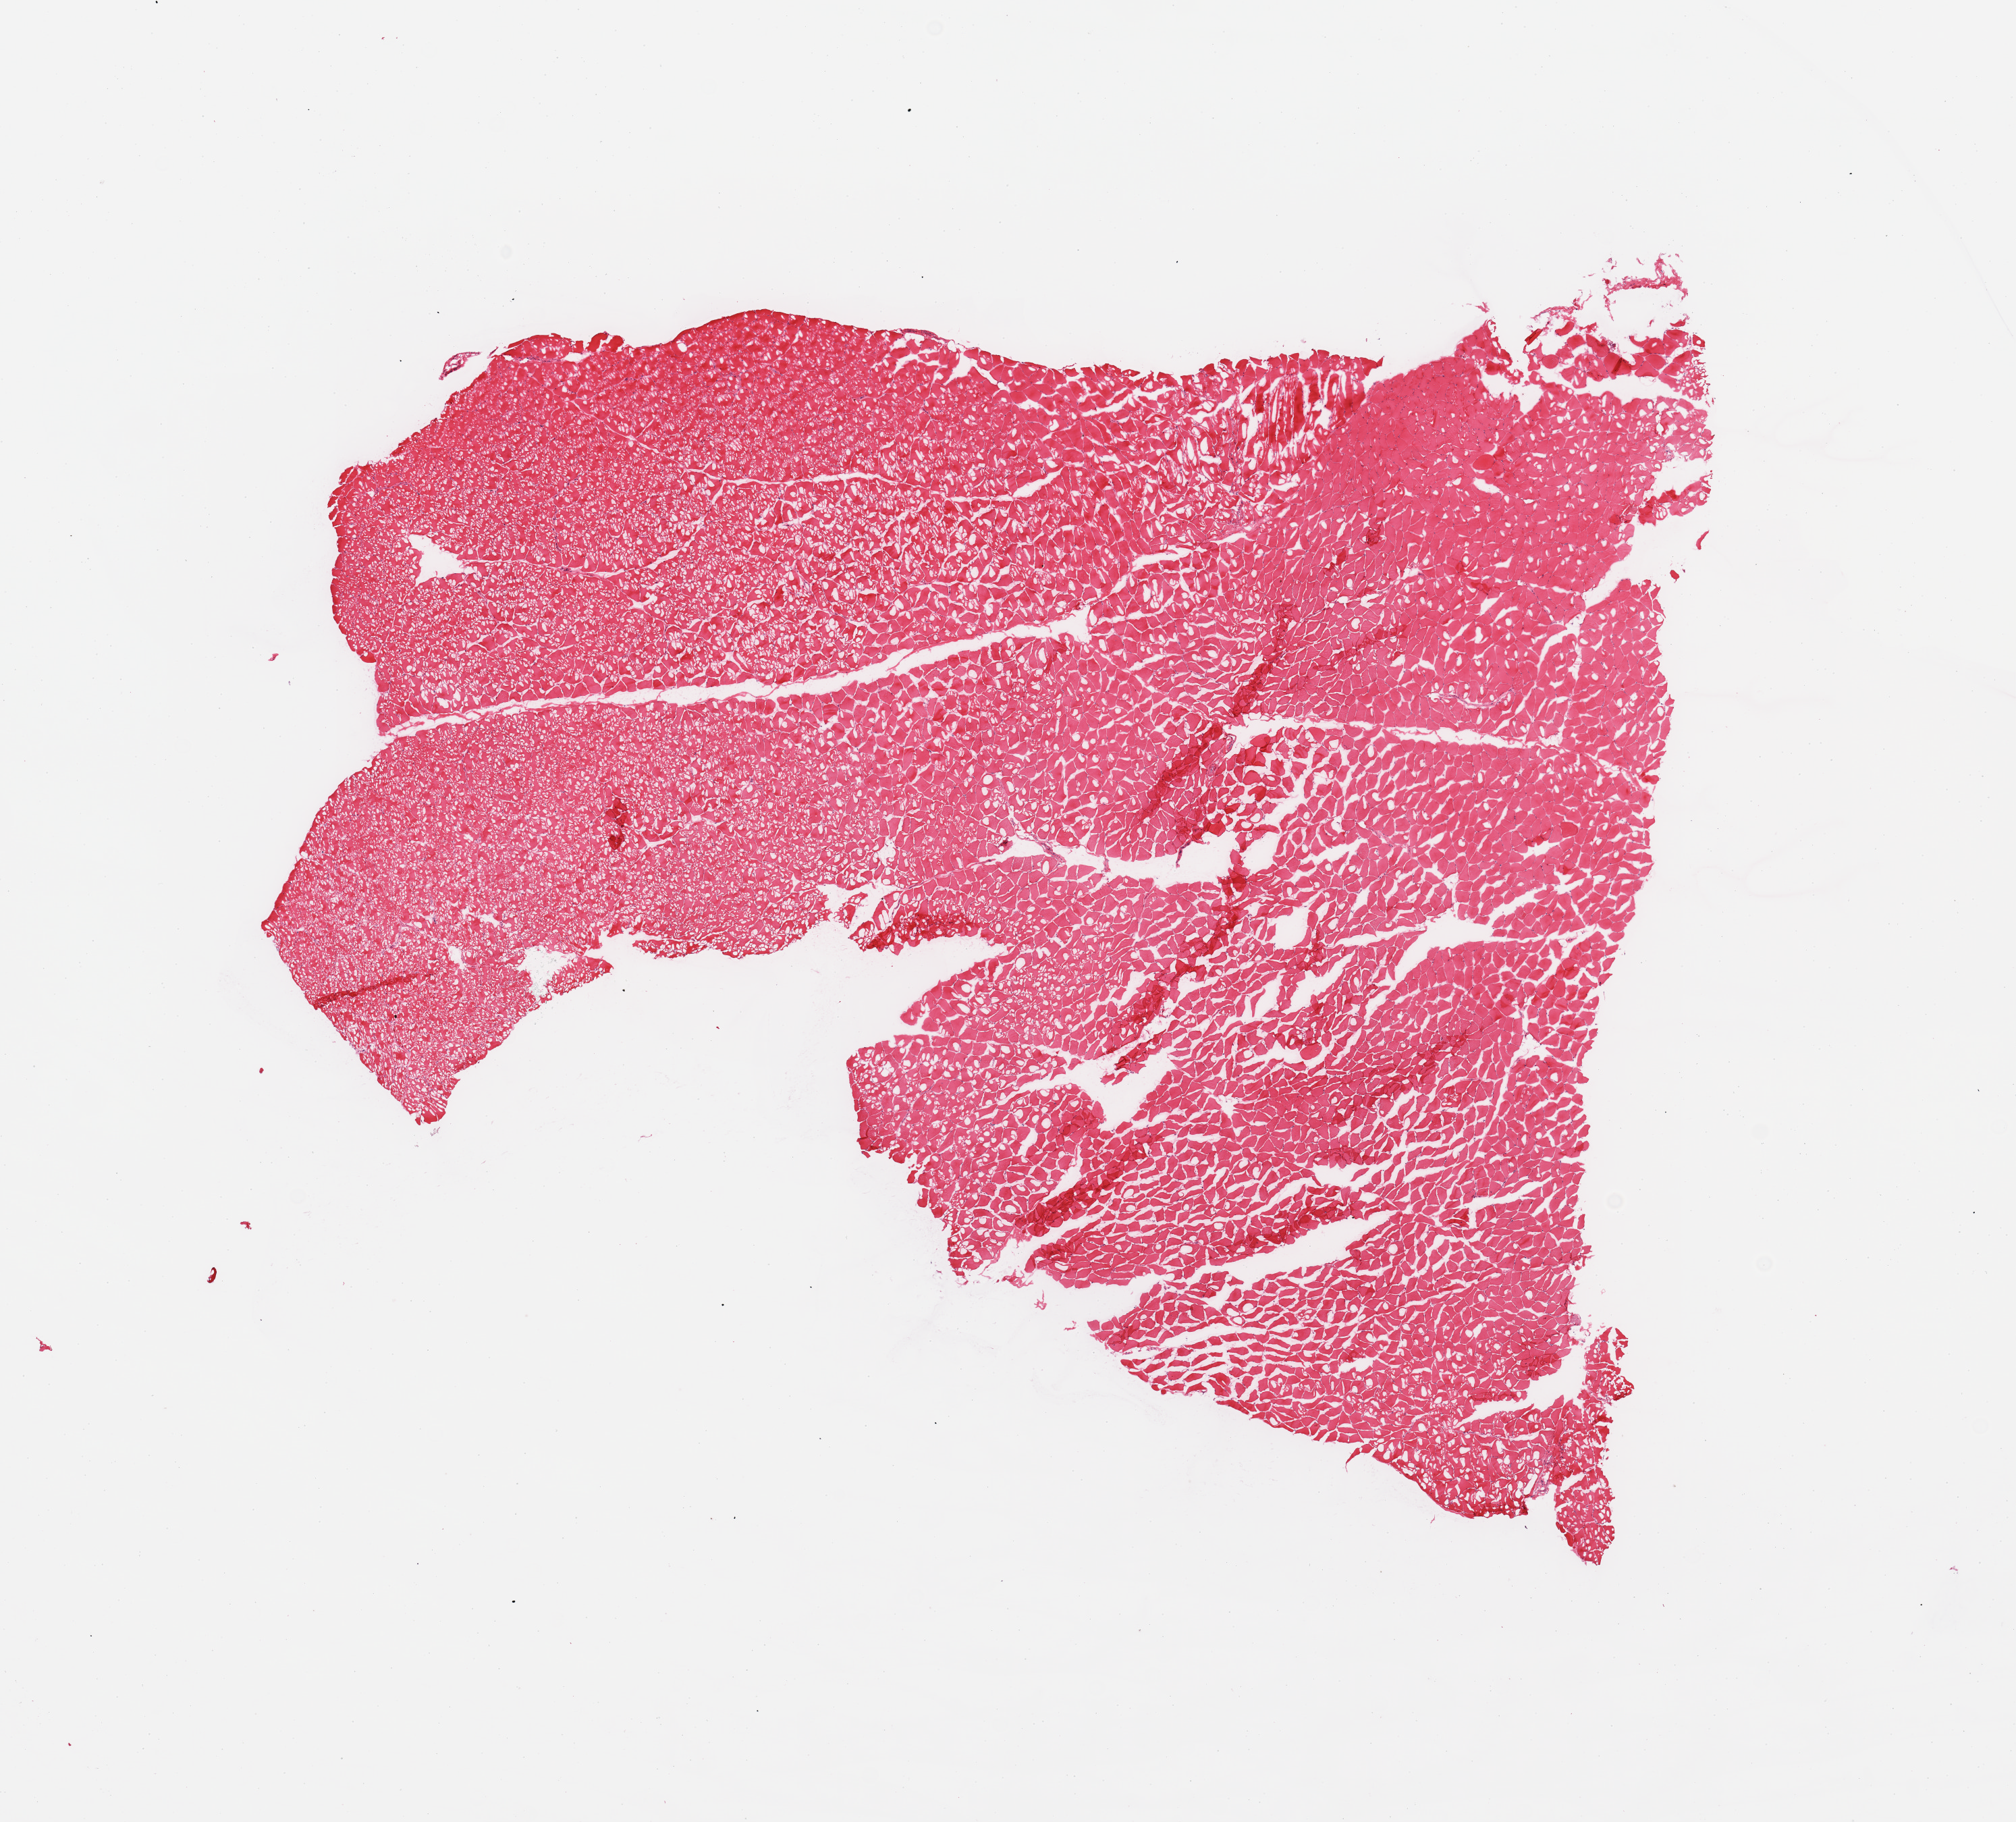
Whole-slide image, haematoxylin and eosin stain, brightfield — shown as a low-resolution overview of the whole scanned area (about 11.8 x 10.7 mm); frozen section; target tissue: skeletal muscle; tissue donor sample. Male donor.
- review note (as recorded): 1 piece